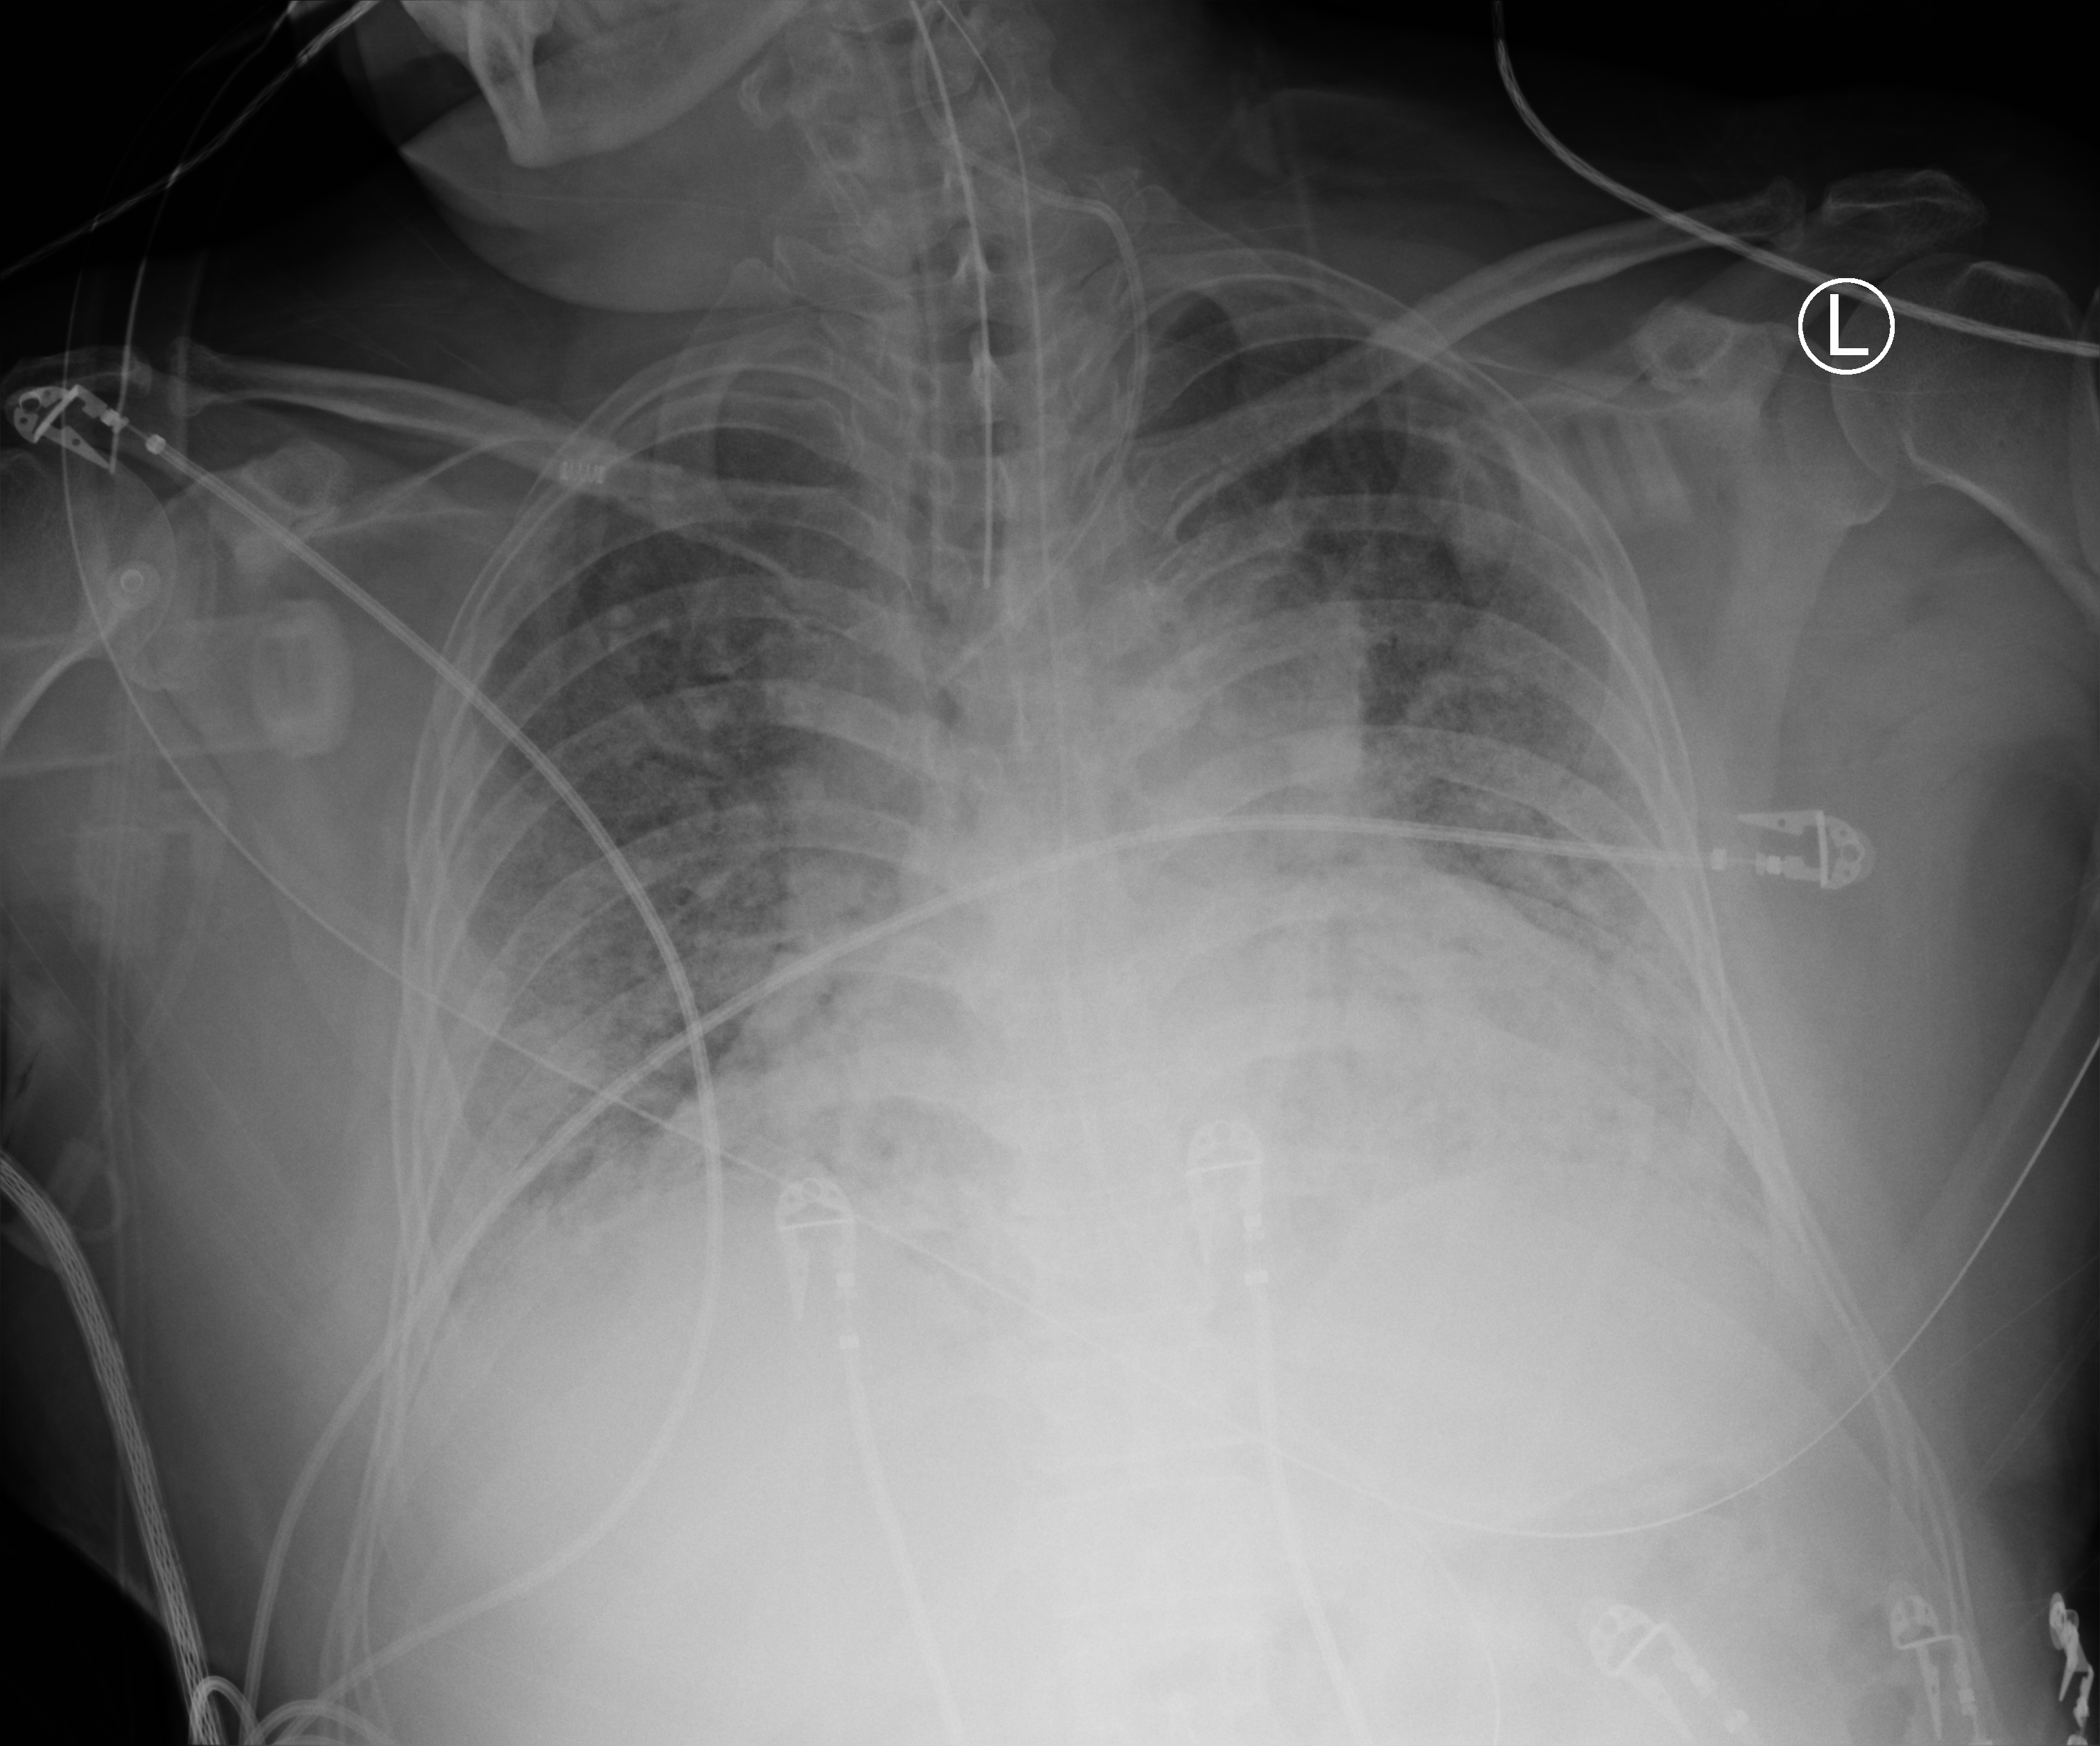
Portable chest radiograph, anteroposterior (AP) projection. Adult patient hospitalised with COVID-19, age 18–59 years.
Admission-level facts for this patient (not findings on this image; timing relative to this image not recorded): diabetes (admission record): no; mechanically ventilated during this hospital stay: yes.